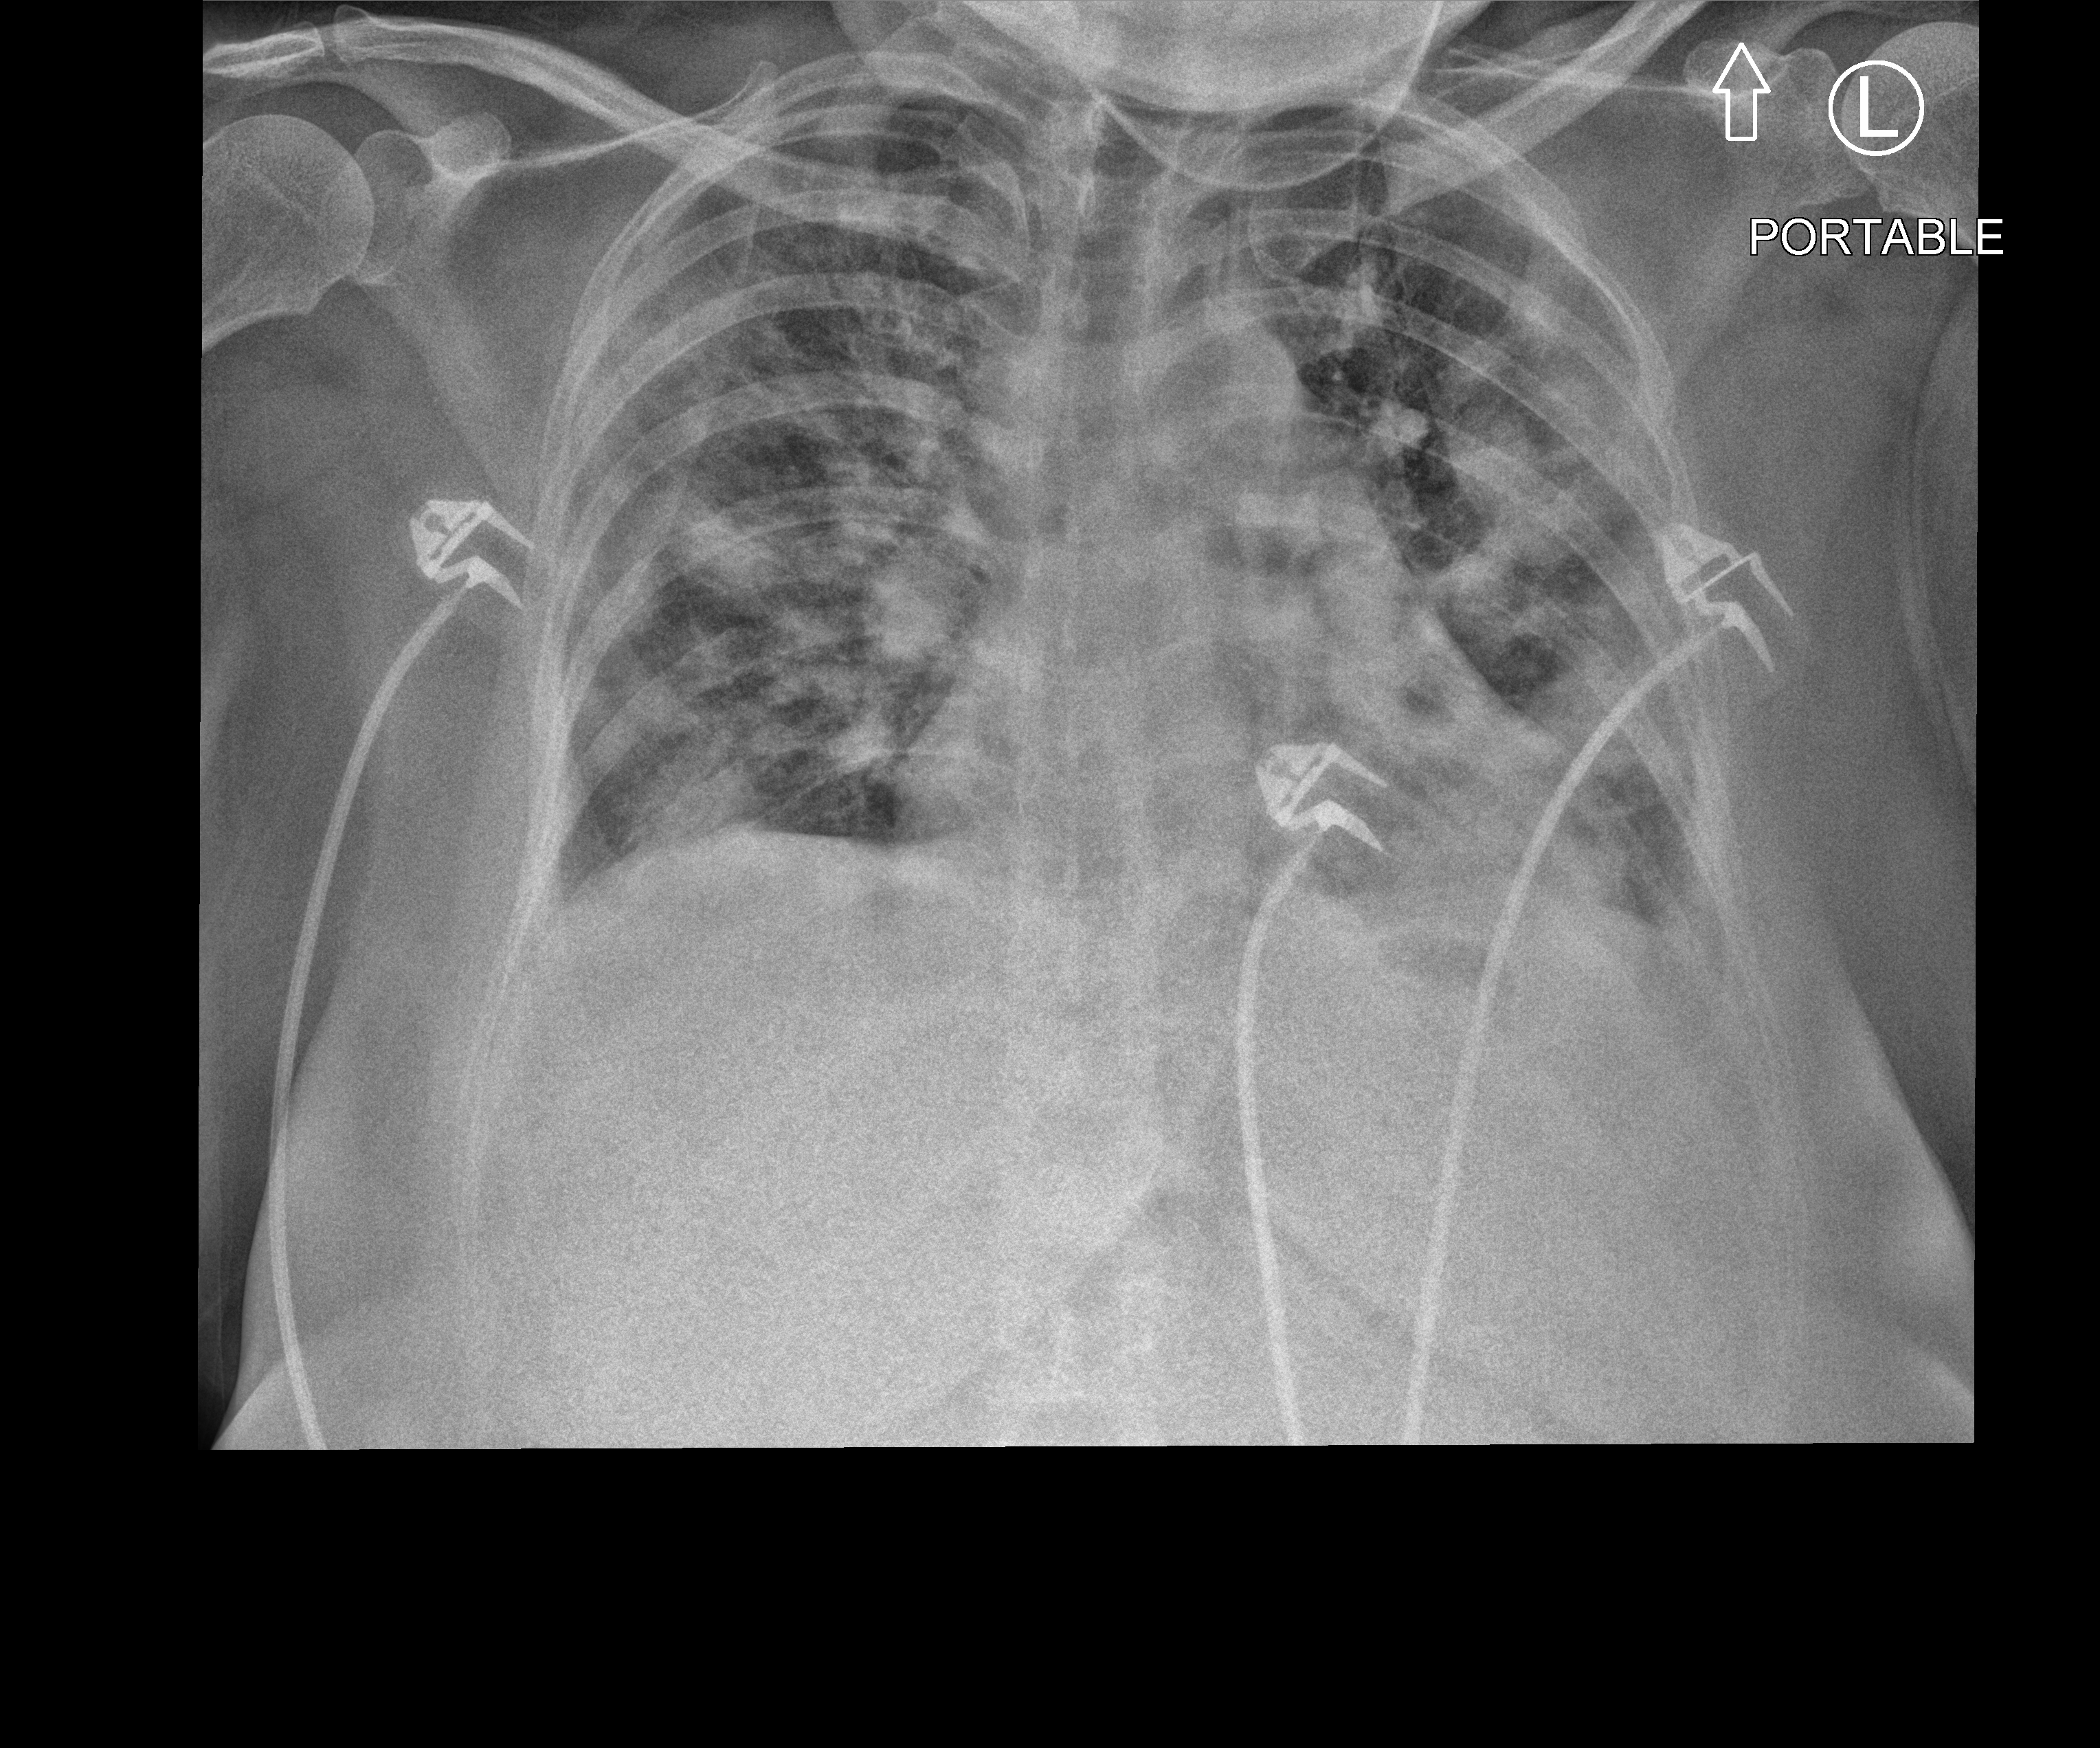
Portable chest radiograph, anteroposterior (AP) projection. Adult patient hospitalised with COVID-19, age 18–59 years.
From the hospital-stay record, not from the radiograph (when in the stay this image was taken is not recorded): mechanically ventilated during this hospital stay: yes; admitted to intensive care during this hospital stay: yes.